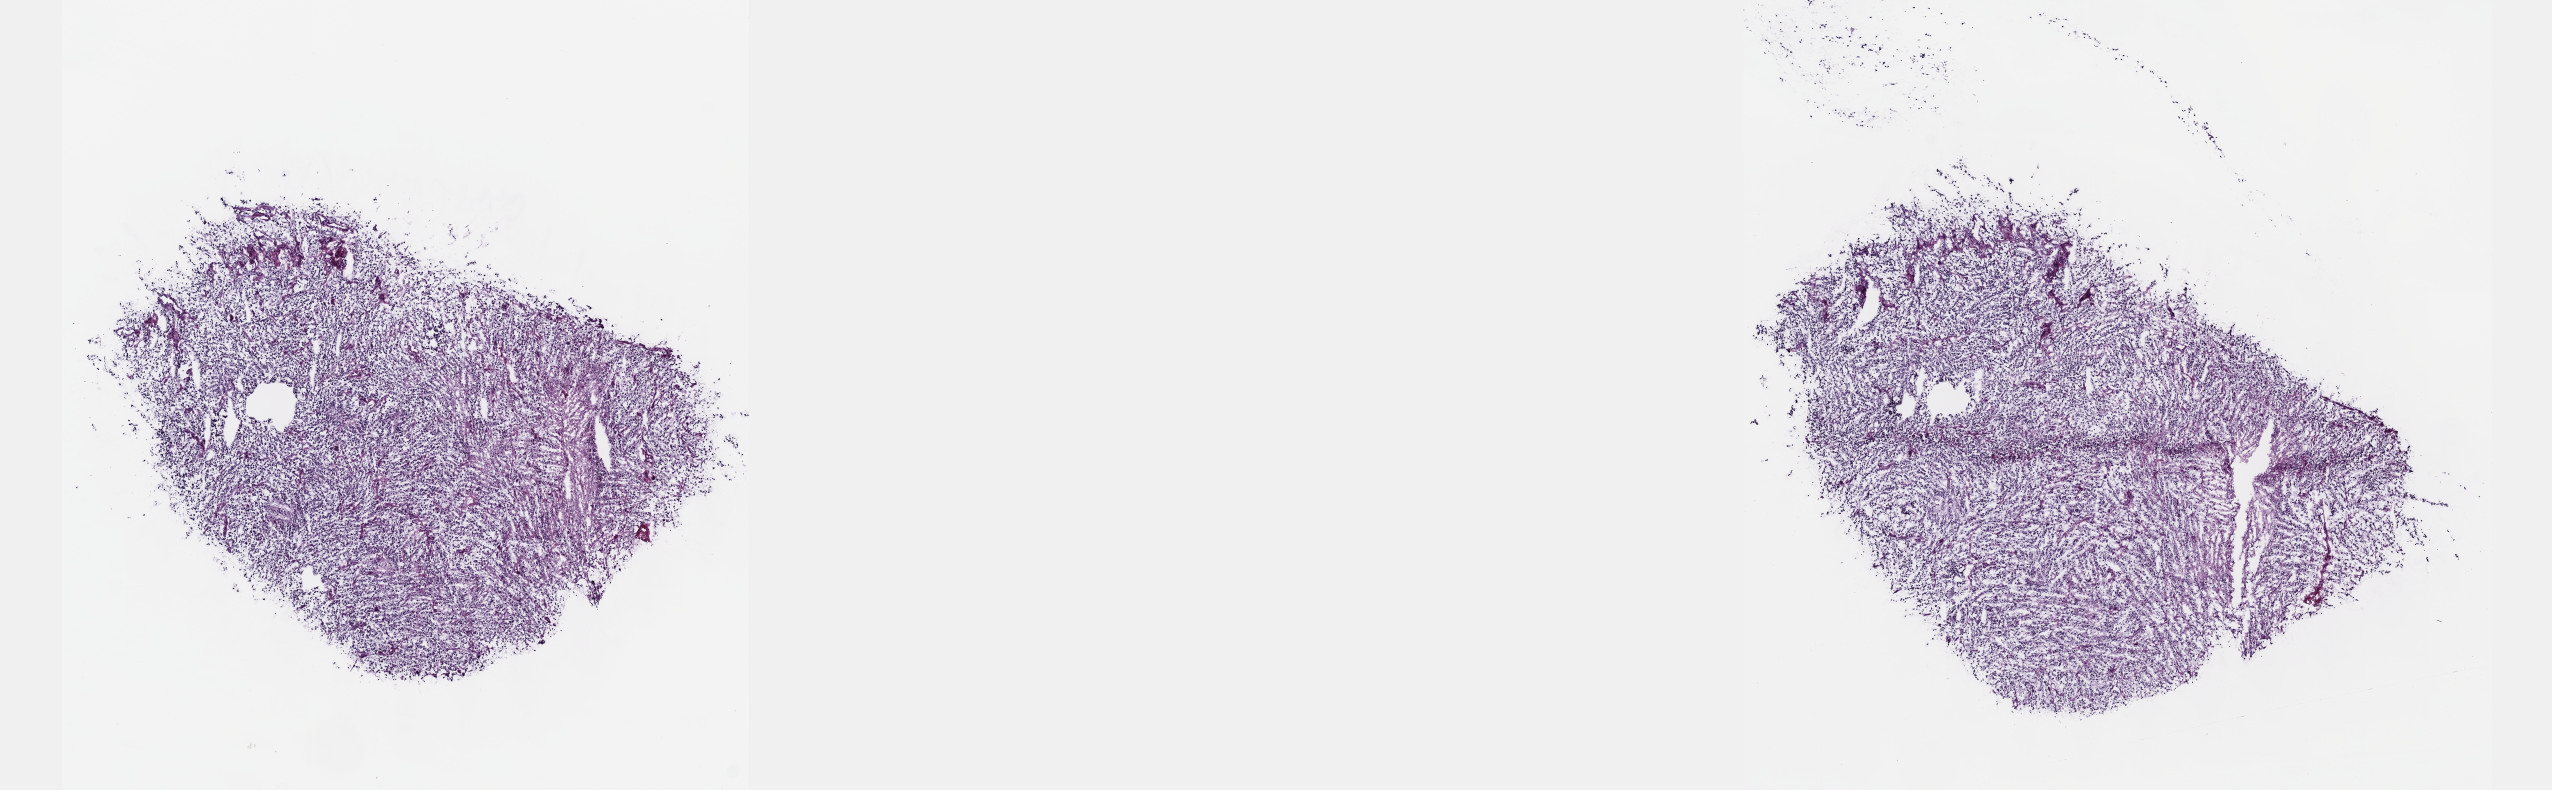
Digitized H&E tissue section (whole slide) — whole scanned area (about 20.6 x 6.4 mm, from a 40x scan) shown as a low-resolution overview. Frozen section from the top of the tissue portion. Primary tumour sample from the brain. Male patient; age at initial diagnosis 63 years. Histologic grade: G3 (poorly differentiated). Slide review estimates, as recorded: tumour cells 80%, tumour nuclei 90%, normal cells 5%, stromal cells 15%, necrosis 0%. Inflammatory infiltration, as recorded: lymphocyte infiltration 0%, monocyte infiltration 0%, neutrophil infiltration 0%.
Diagnosis: Oligodendroglioma, anaplastic (cerebrum).